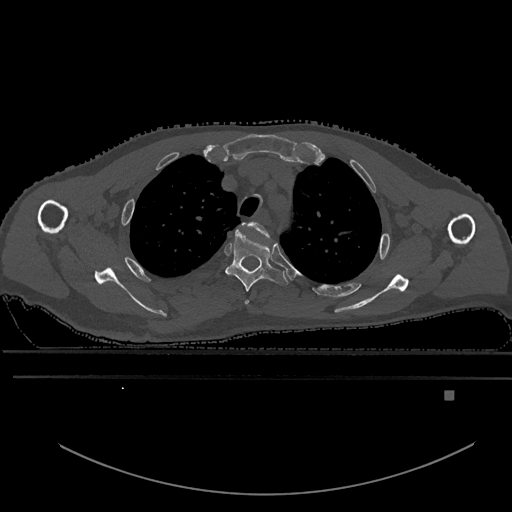
CT including the spine, one axial slice. Bone window (W 1800 / L 400 HU). 0.5 mm slice thickness. 512 × 512 image matrix, field of view 456 × 456 mm. Patient: male, 82 years. From the clinical record (not read from this slice): primary cancer: prostate.
Structures marked on this image (semi-automatically segmented with operator editing):
- T2 vertebra: bounding box <240,222,269,305> (left, top, right, bottom; pixels)
- T3 vertebra: <225,232,289,292>